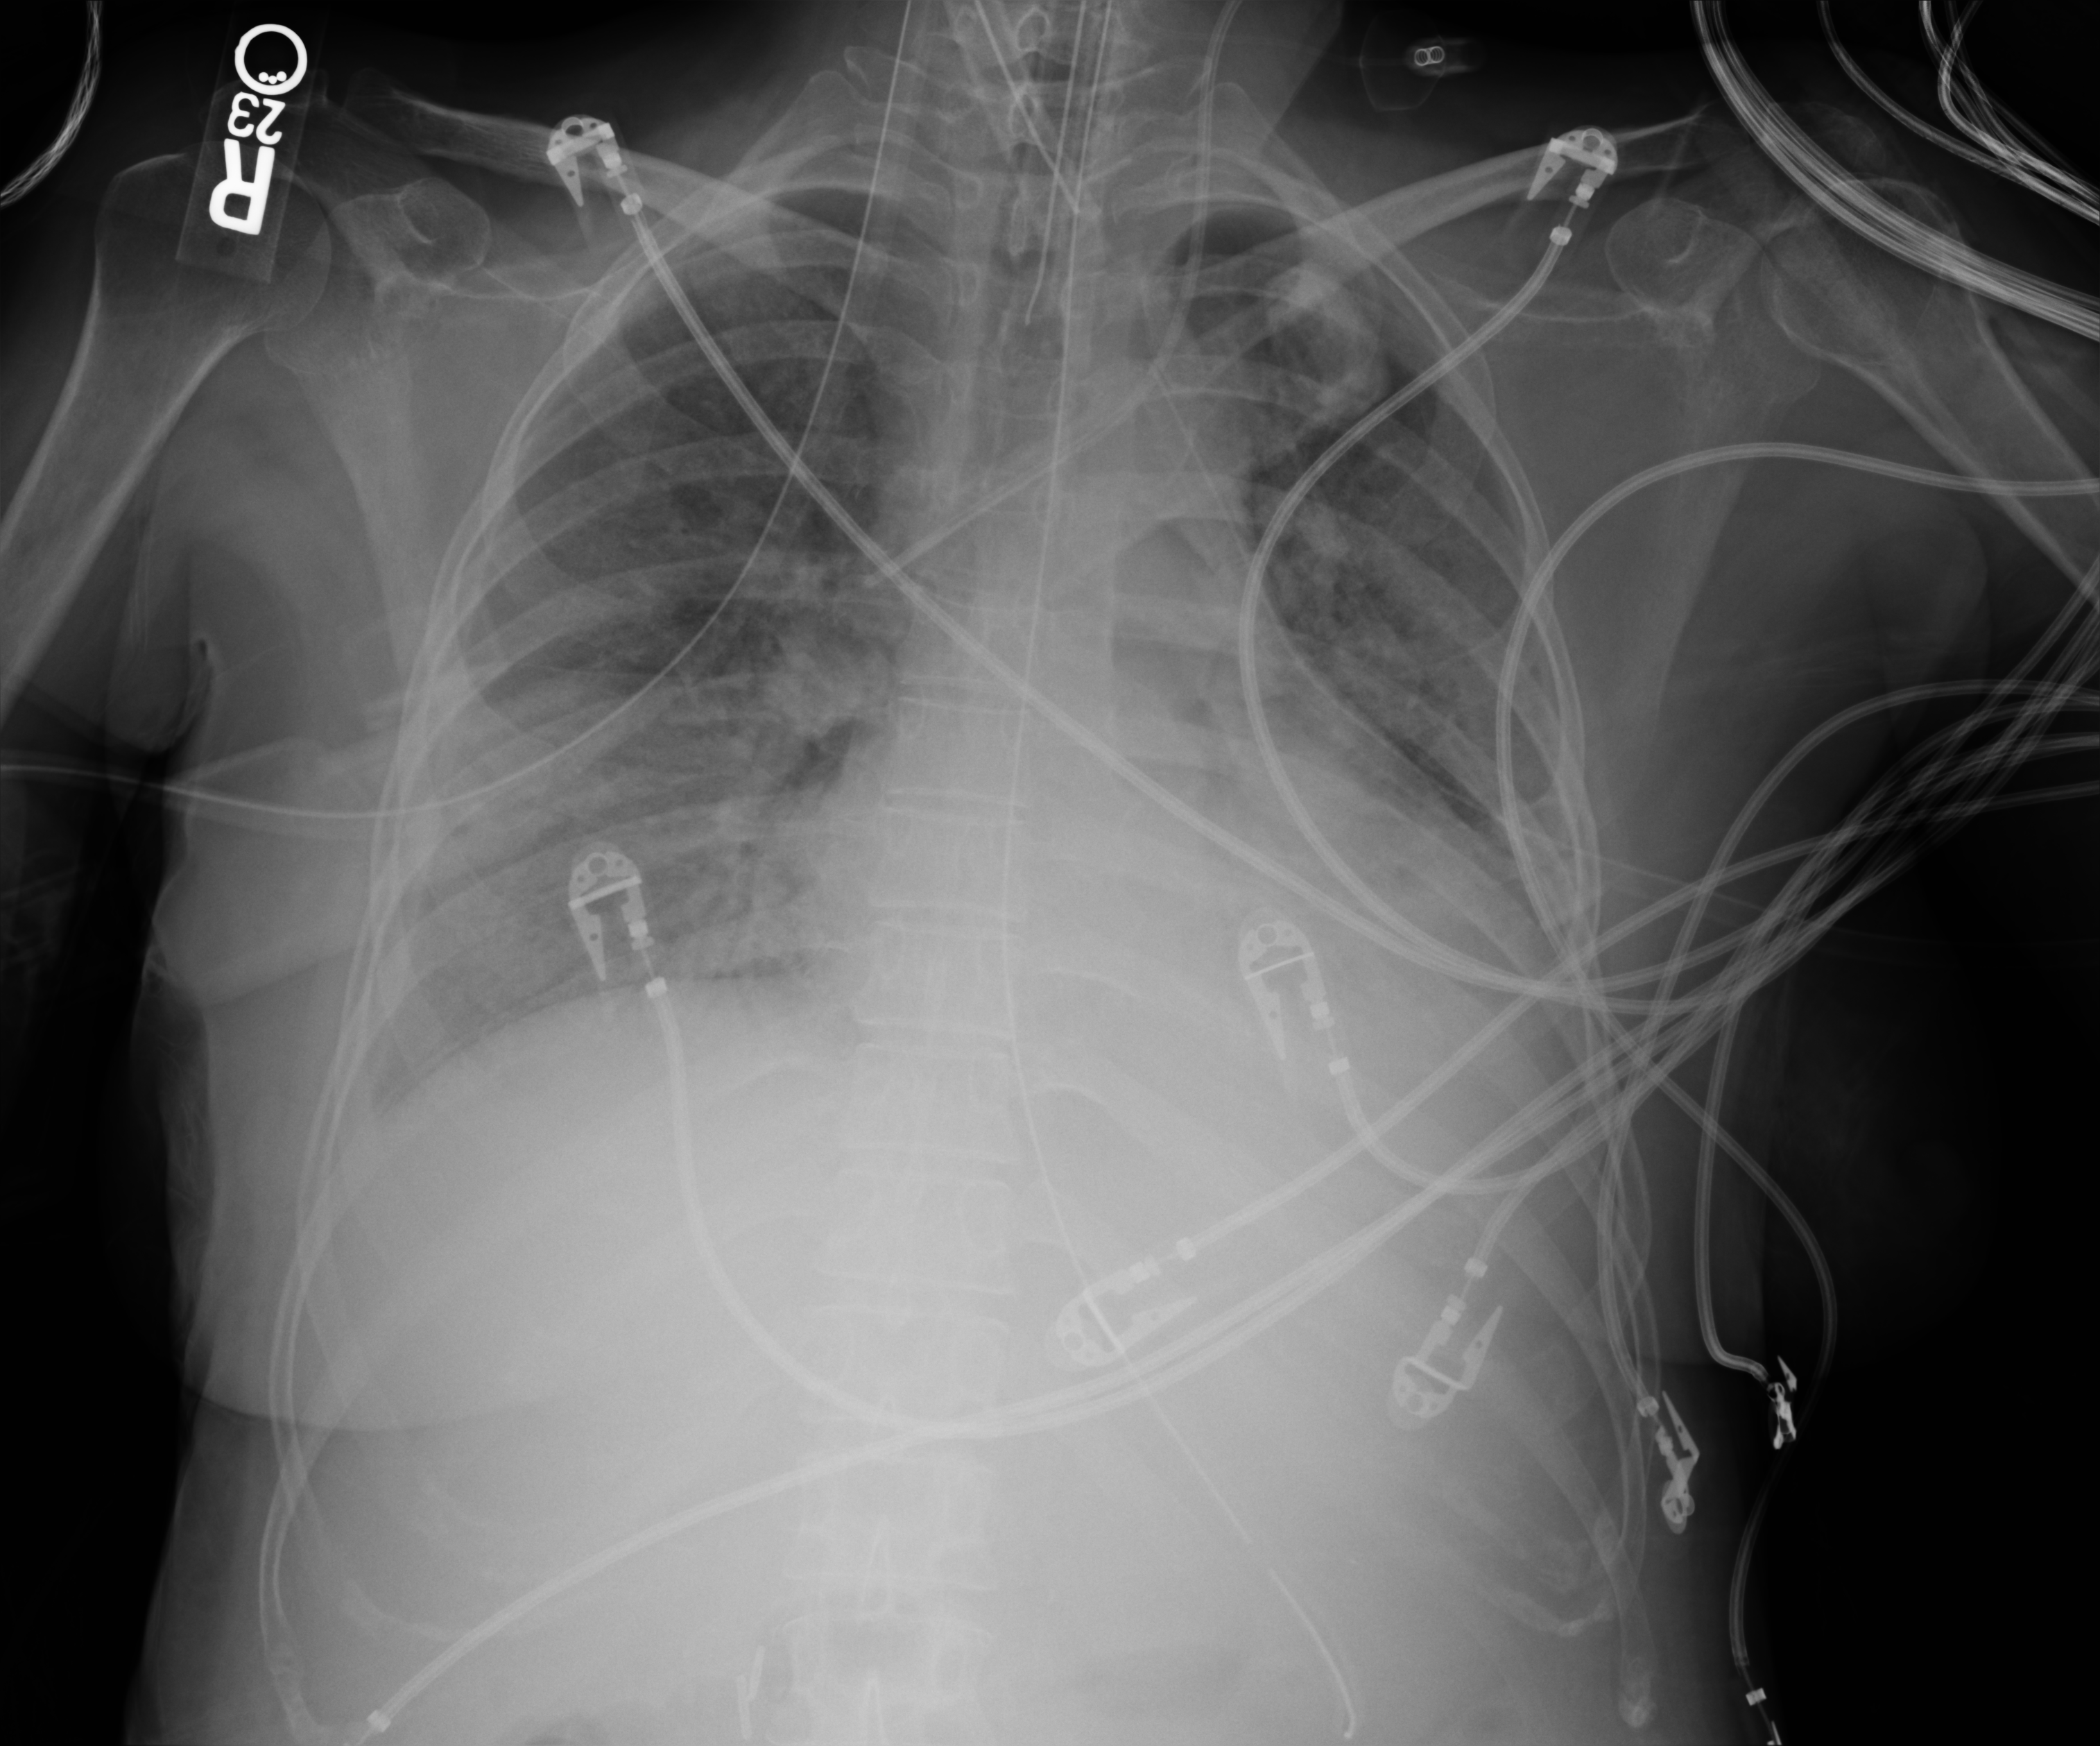
Bedside chest radiograph (computed radiography), anteroposterior (AP) projection. Adult patient hospitalised with COVID-19, age 18–59 years.
From the hospital-stay record, not from the radiograph (when in the stay this image was taken is not recorded): admitted to intensive care during this hospital stay: yes; length of hospital stay: 10 days.